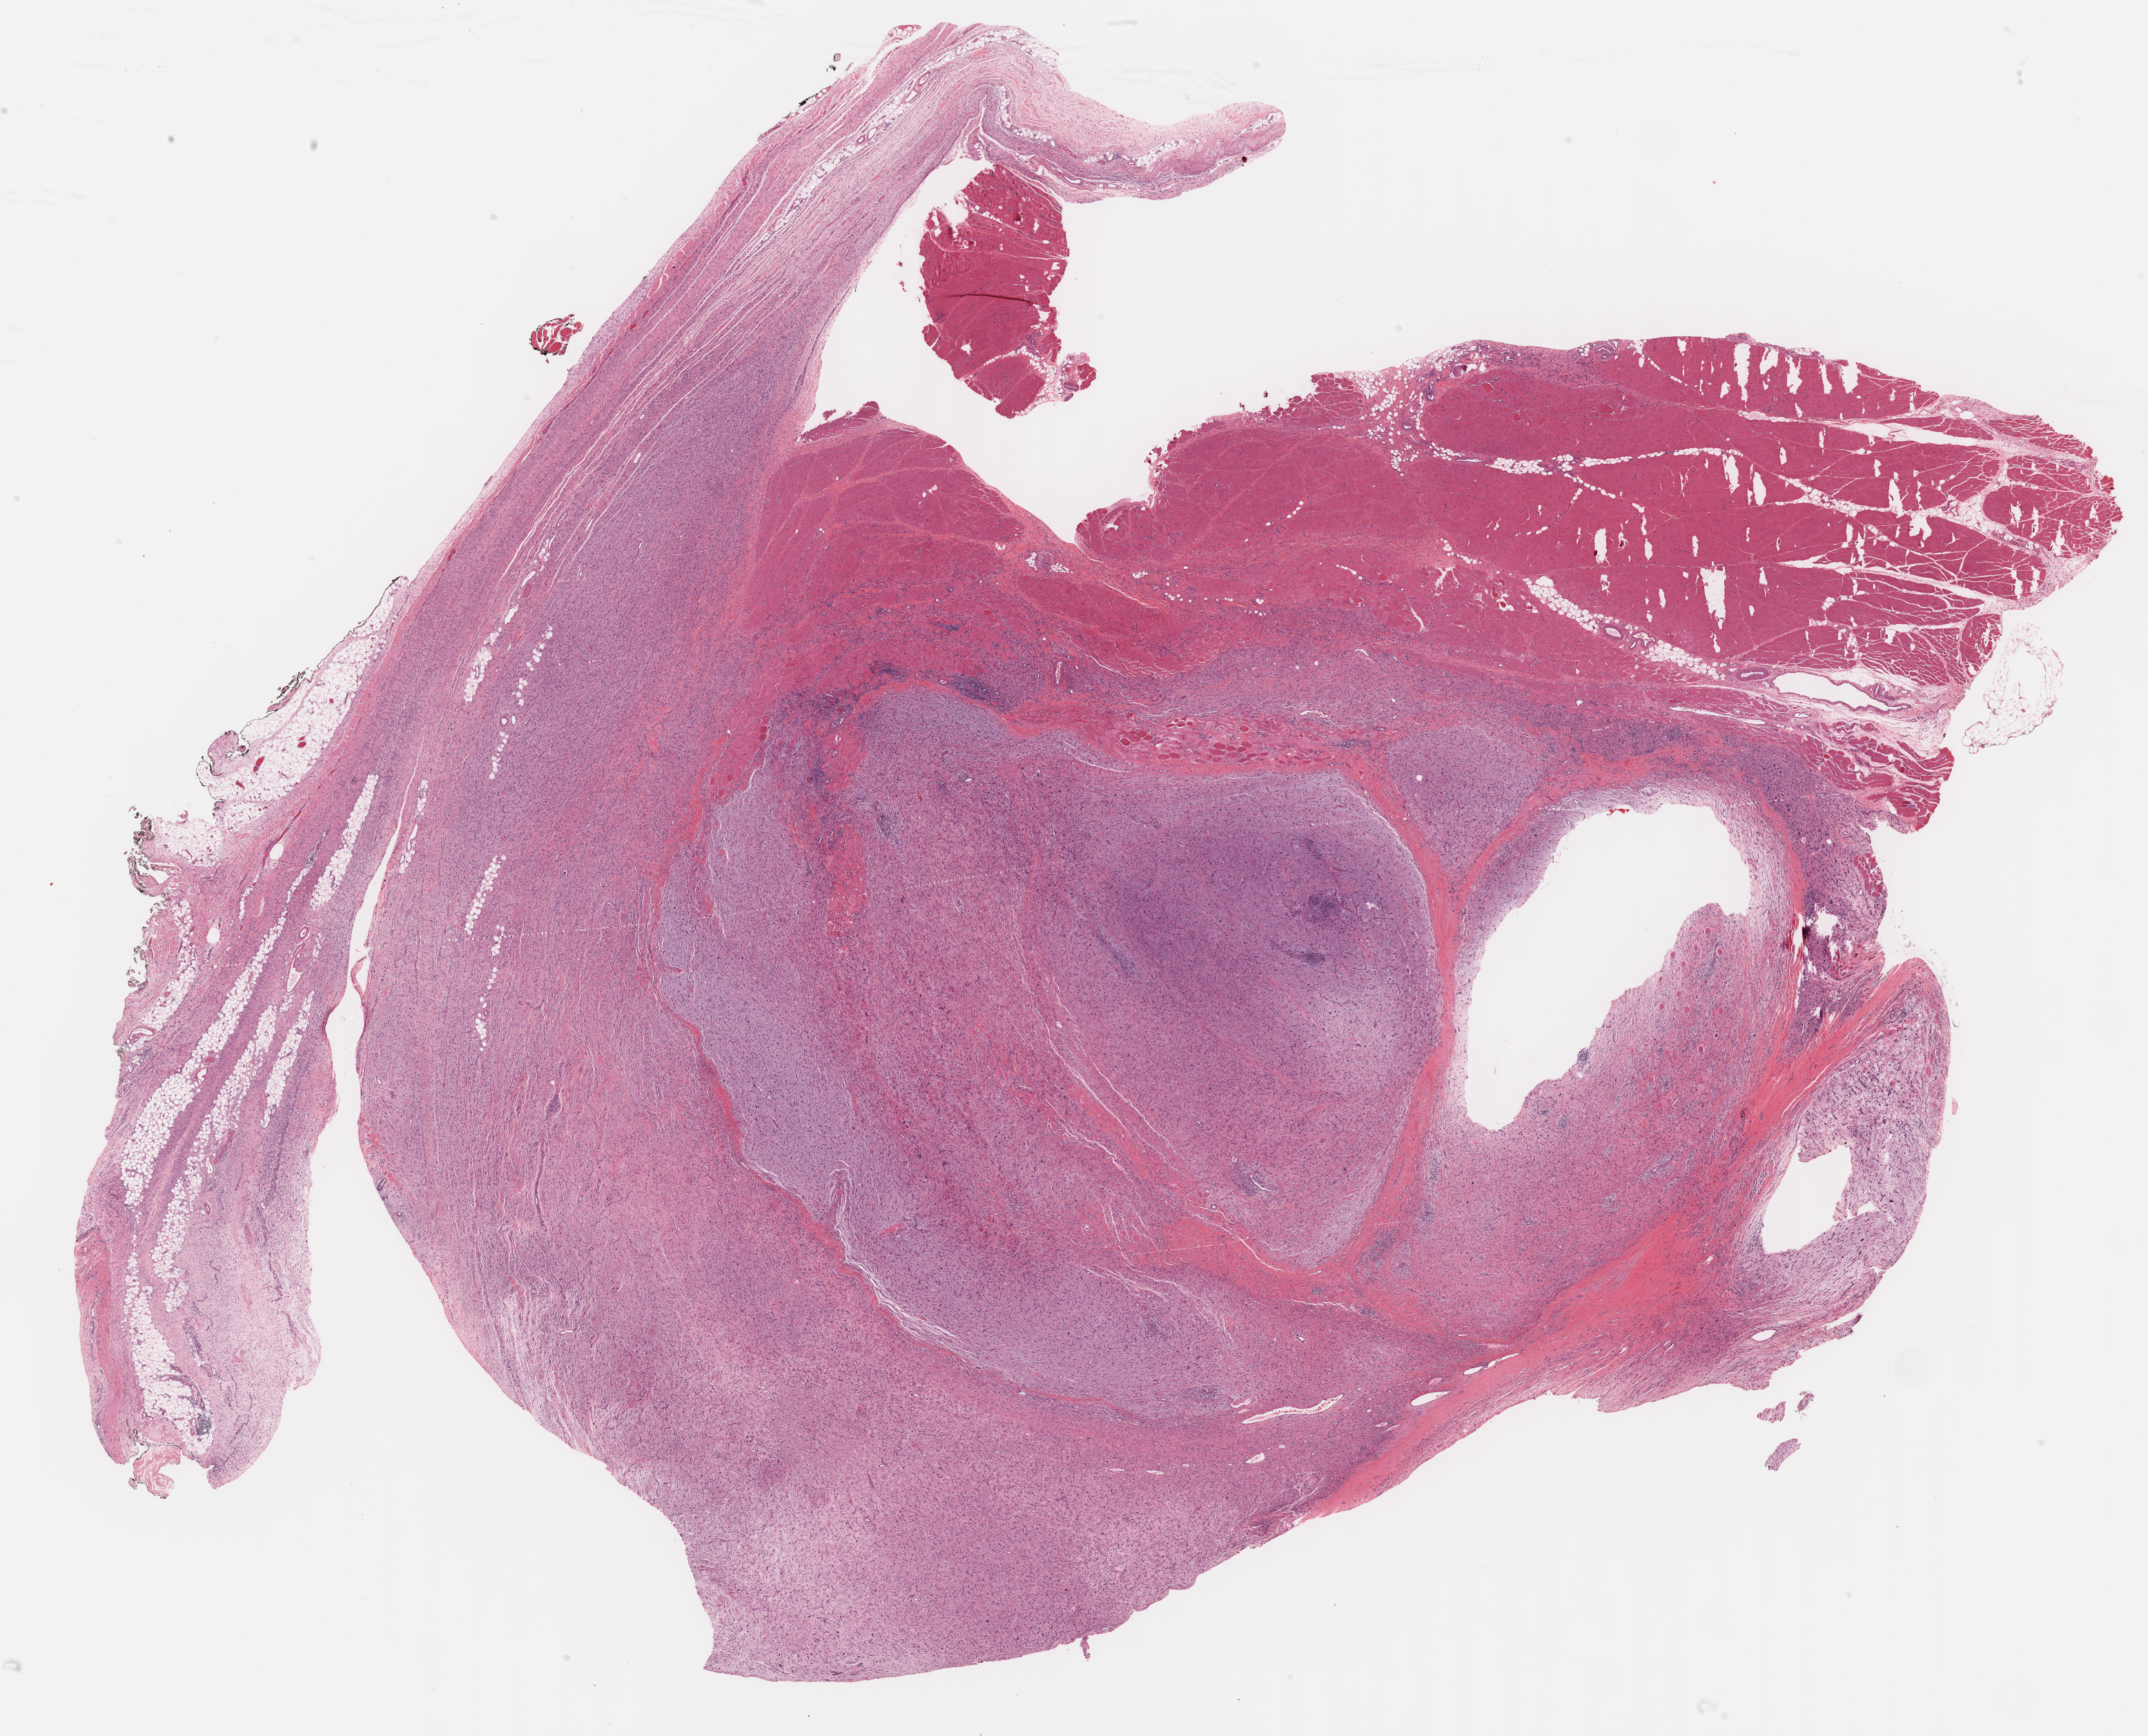
Digitized Hematoxylin and eosin (H&E) stained tissue section (whole slide) — a low-resolution overview of the entire scanned area, about 25.2 x 20.3 mm; FFPE section; primary tumour sample from the connective, subcutaneous and other soft tissues. Female, age 78 years at initial diagnosis.
* pathologic diagnosis: Fibromyxosarcoma (connective, subcutaneous and other soft tissues of lower limb and hip)